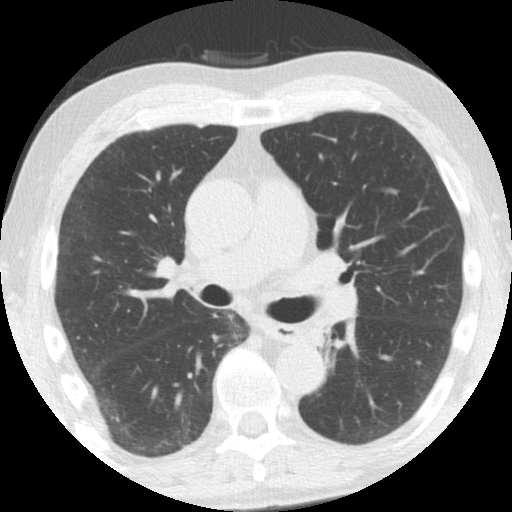
Low-dose screening chest CT, axial slice. Third annual screen. Lung window (W 1500 / L -600 HU). Slice 53 of 108 in the series. 512 × 512 image matrix. Male participant, aged 61 years at enrolment. Former smoker at enrolment.
Lesion marked by an expert reader, bounding box (x1, y1, x2, y2) in pixels: (293, 316, 344, 362). No non-calcified nodule or mass ≥4 mm was recorded by the screening reader at this exam. Official screen result: negative screen, minor abnormalities not suspicious for lung cancer.